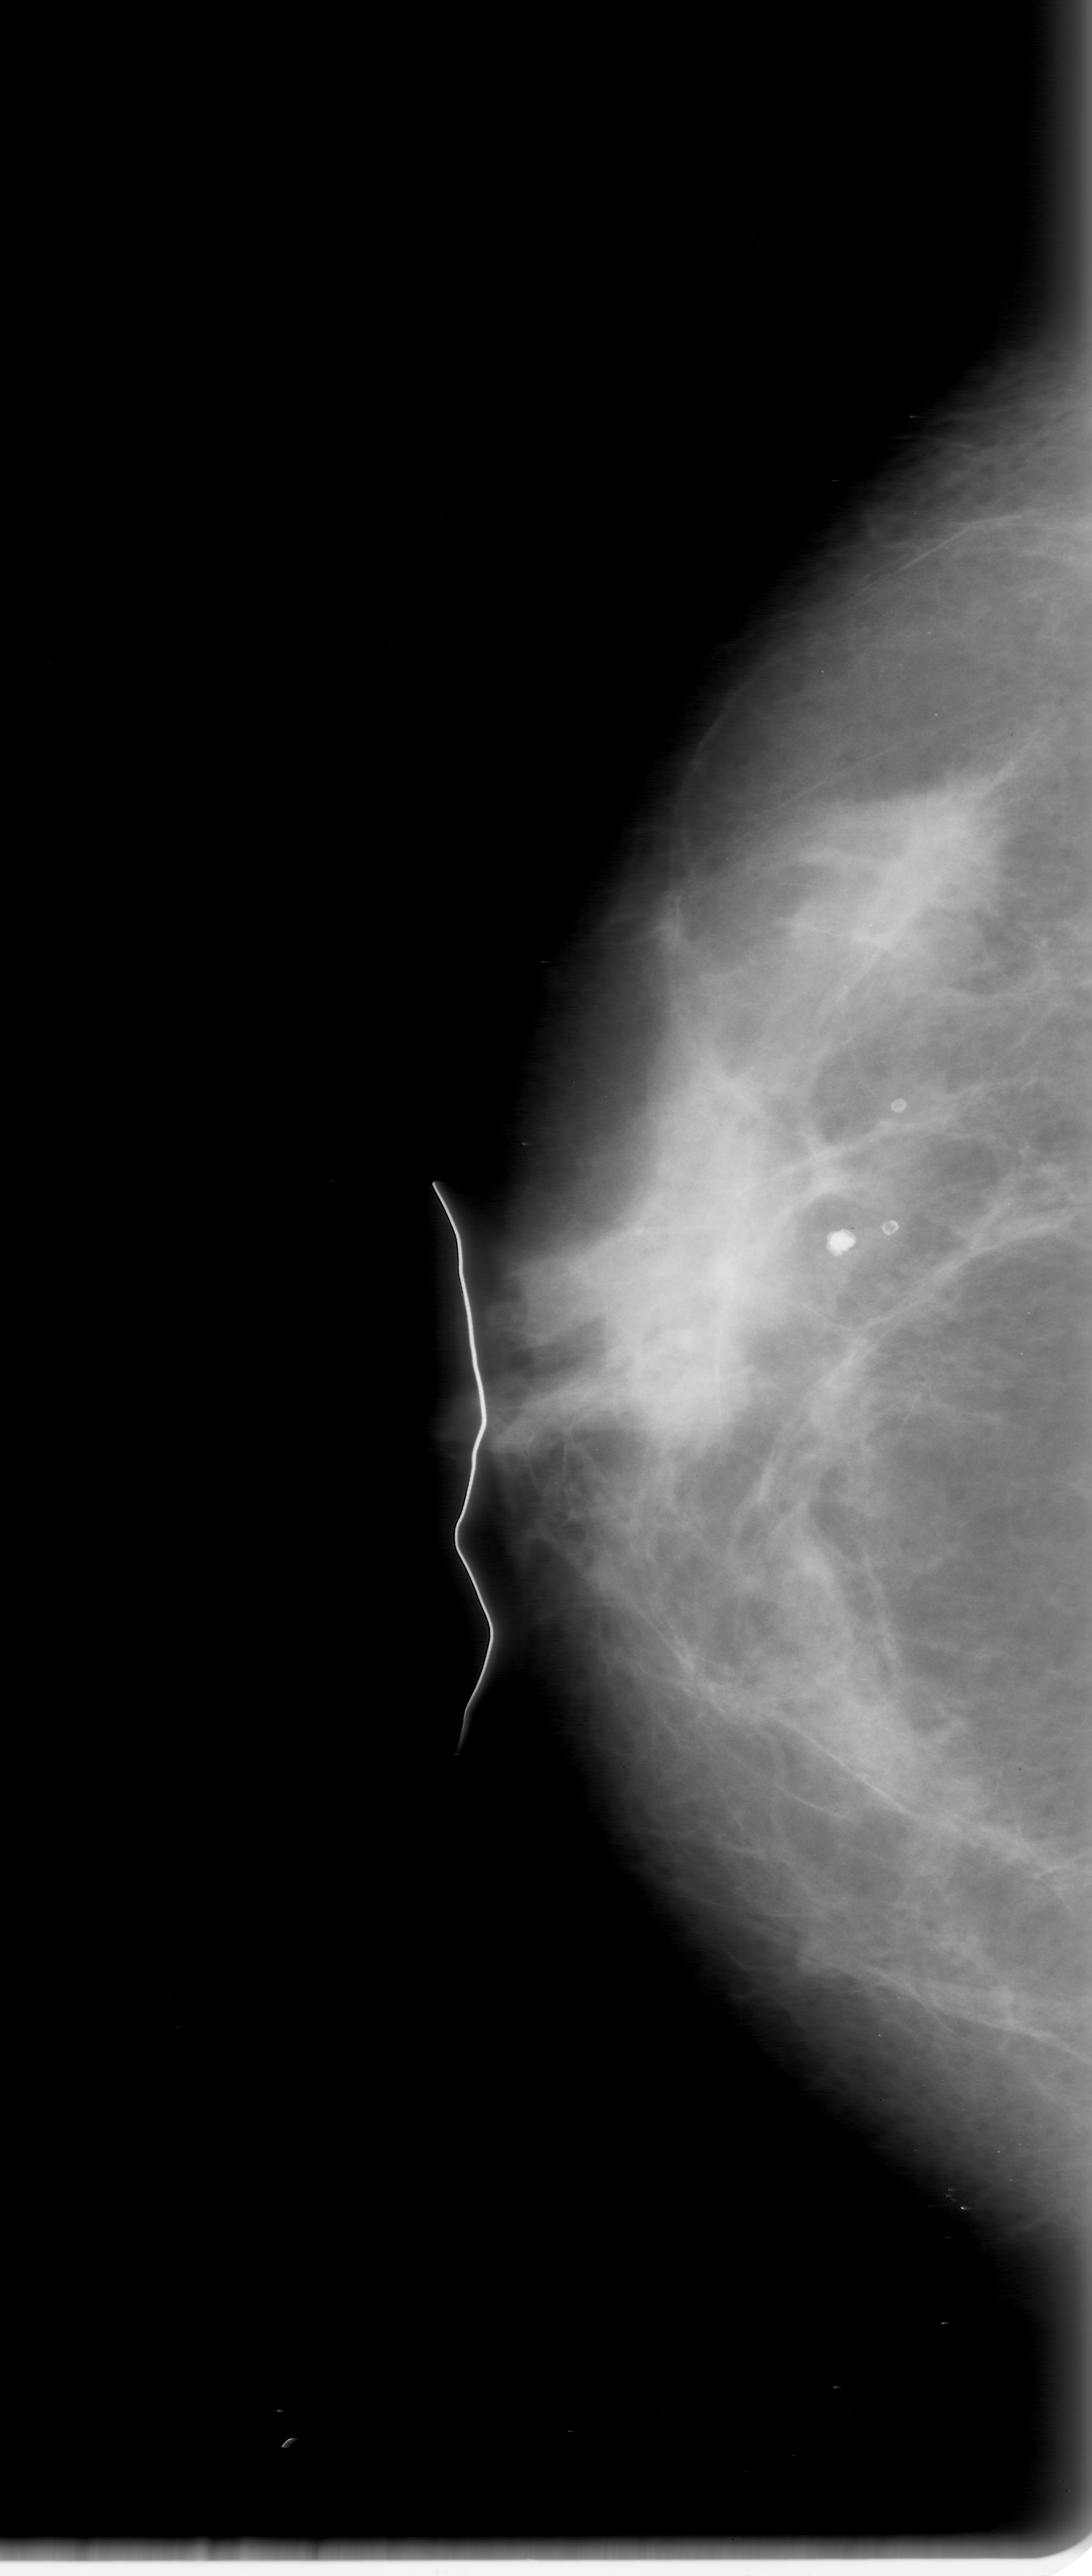
Scanned film-screen mammogram; right breast; CC view; breast composition: heterogeneously dense (BI-RADS density category 3 of 4).
Abnormality record for this image: mass, shape irregular, margins spiculated; BI-RADS assessment category 0 (incomplete: needs additional imaging); pathology (as recorded): malignant.